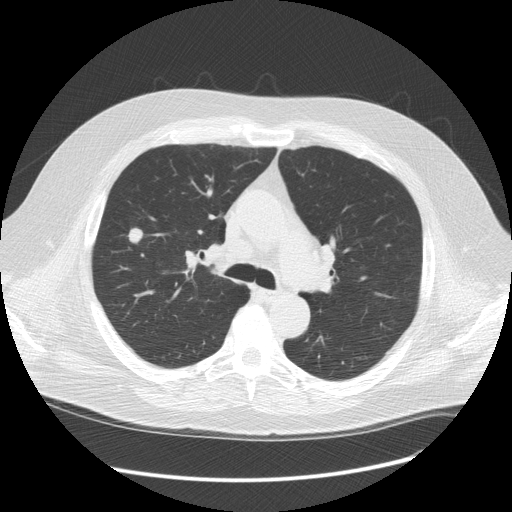
Low-dose screening chest CT, one axial slice; 120 kVp; lung window (W 1500 / L -600 HU); 2.5 mm slice thickness; 512 × 512 image matrix.
Outlined on this slice (outlined manually by an expert reader):
- lesion 1 (tumor, upper lobe of right lung): box from (x=129, y=228) to (x=143, y=243) px